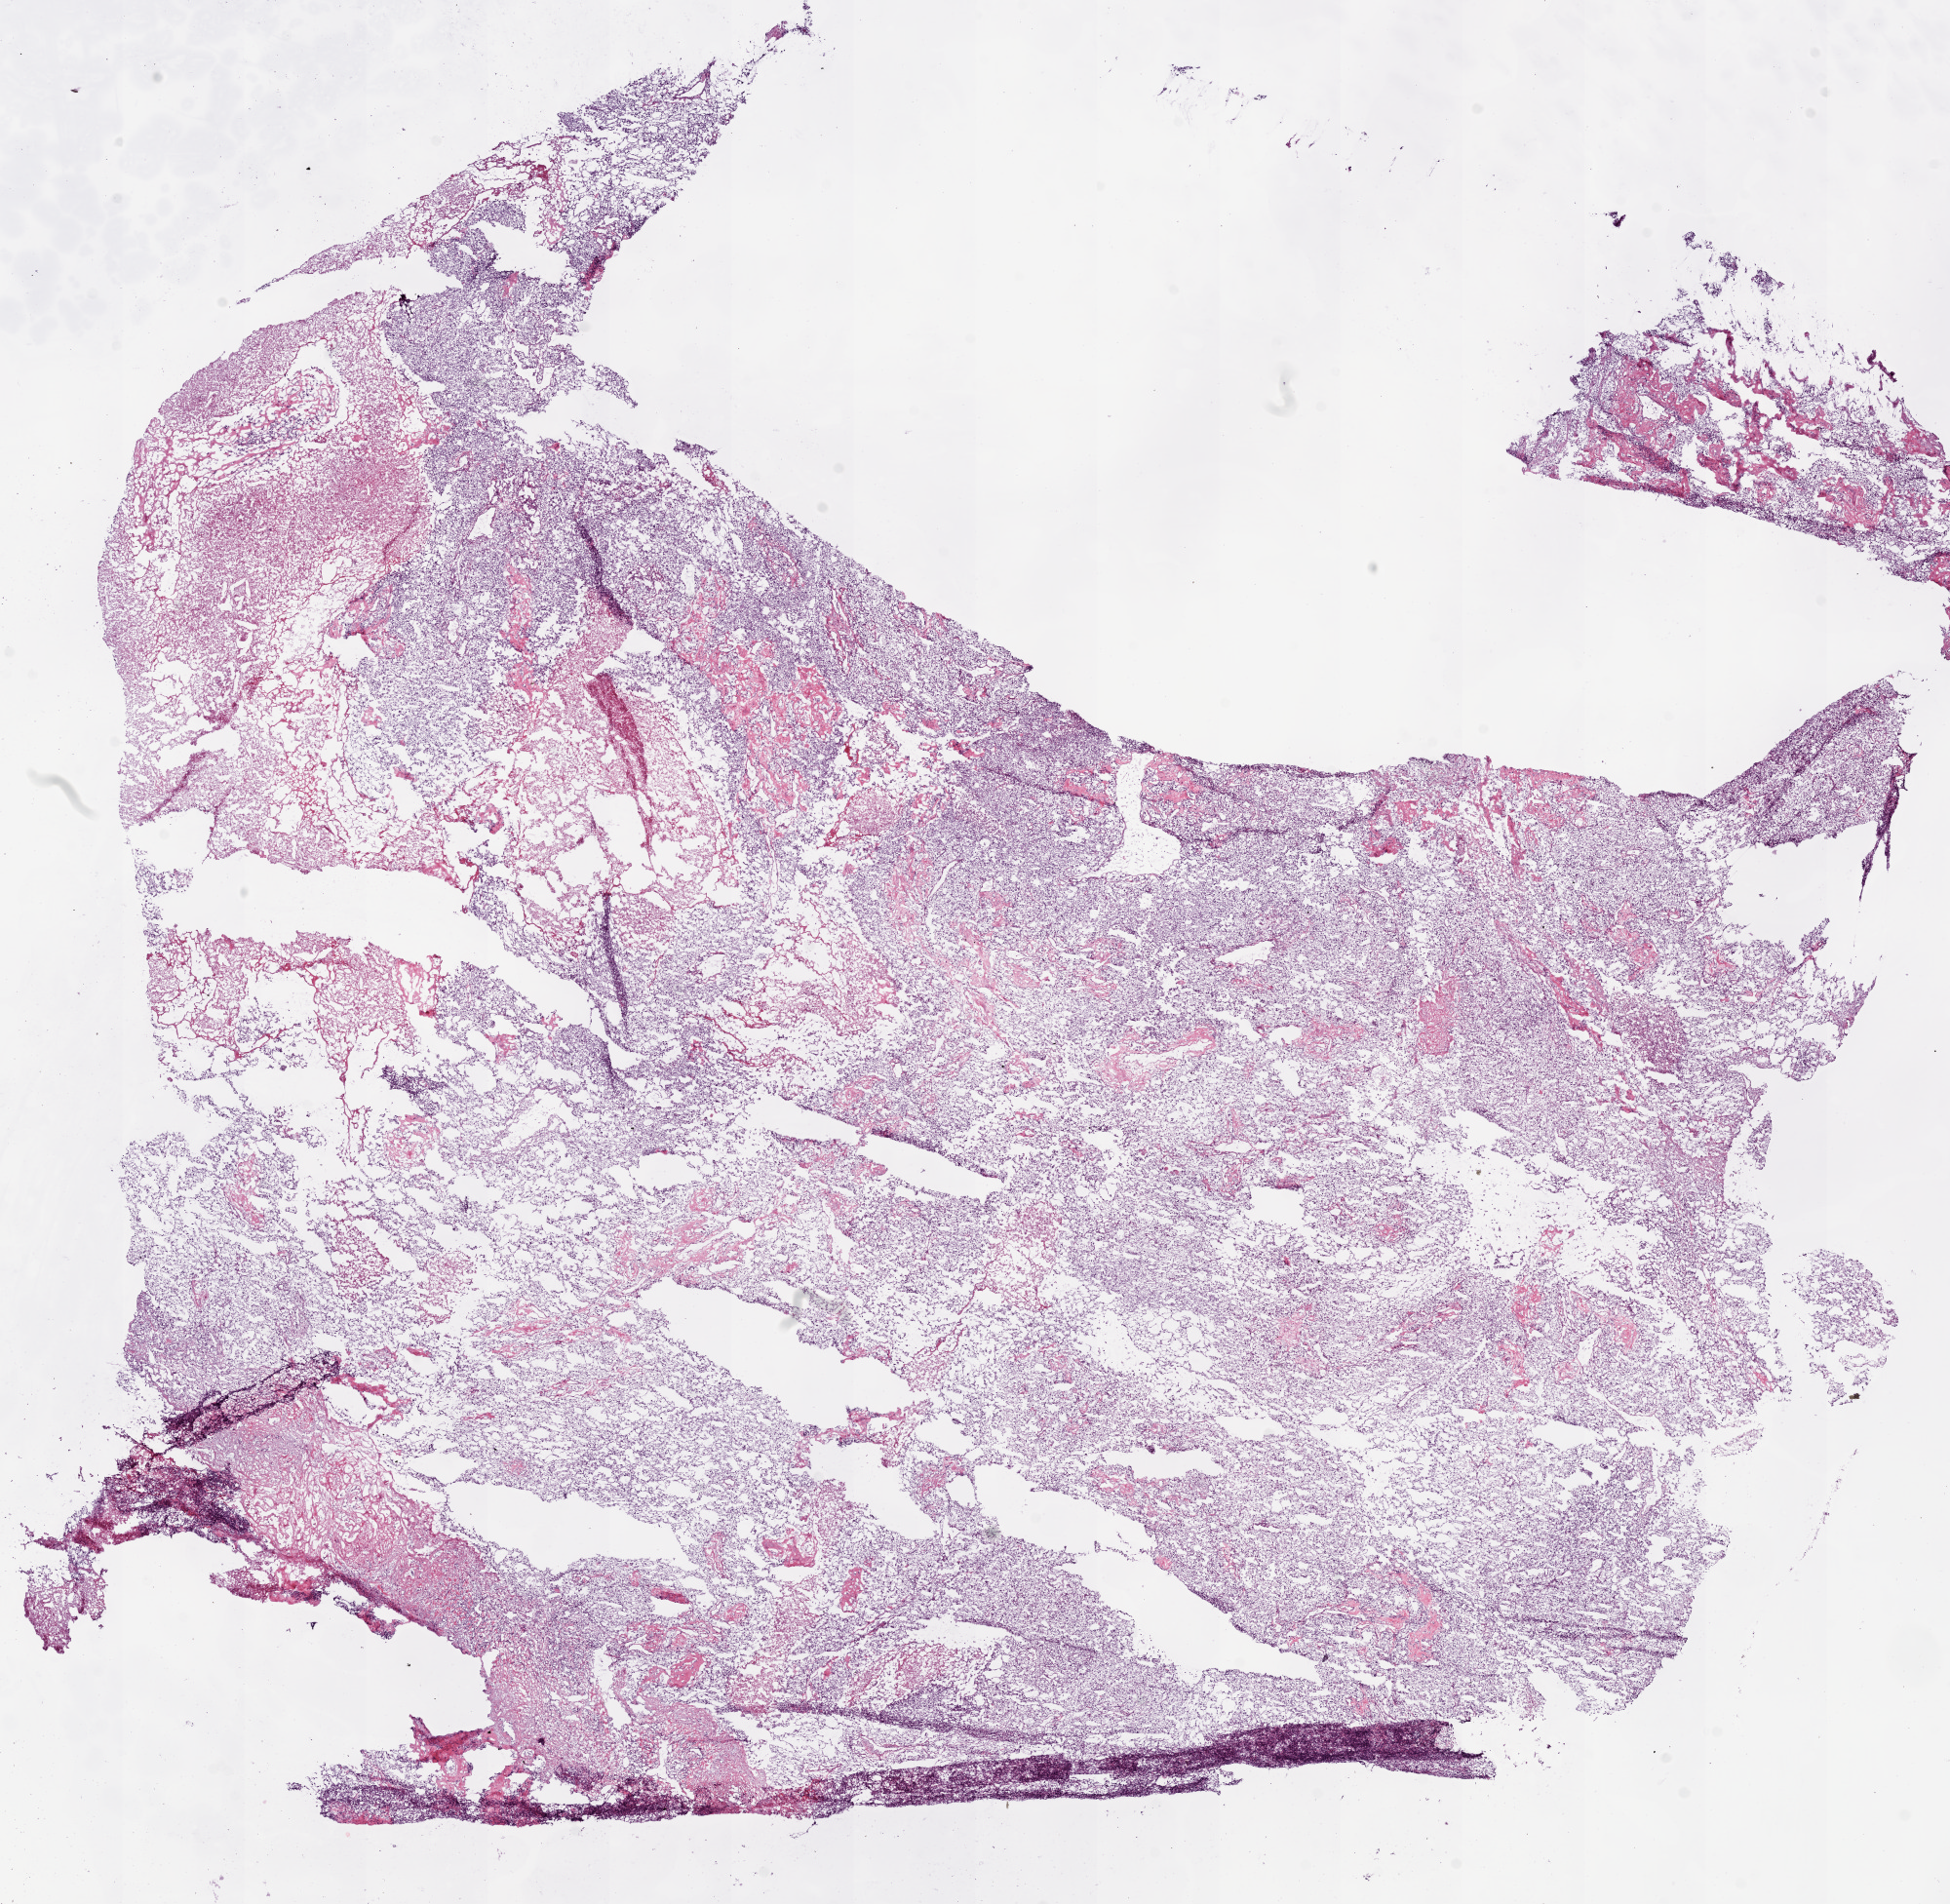
Digitized H&E-stained tissue section (whole slide), shown as a low-resolution overview of the whole scanned area (about 16.0 x 15.7 mm); frozen section from the bottom of the tissue portion; kidney, primary tumour sample. Patient: male, age at initial diagnosis 41 years. Histologic grade: G2 (moderately differentiated). Pathologist review of this section (percent, as recorded): tumour cells 80%, tumour nuclei 85%, normal cells 0%, stromal cells 10%, necrosis 10%. Infiltration values recorded for this section: lymphocyte infiltration 5%, monocyte infiltration 0%, neutrophil infiltration 0%.
Diagnosis: Clear cell adenocarcinoma, NOS. AJCC pathologic stage: II (6th edition). Laterality: left. TNM: T2 N0 M0.